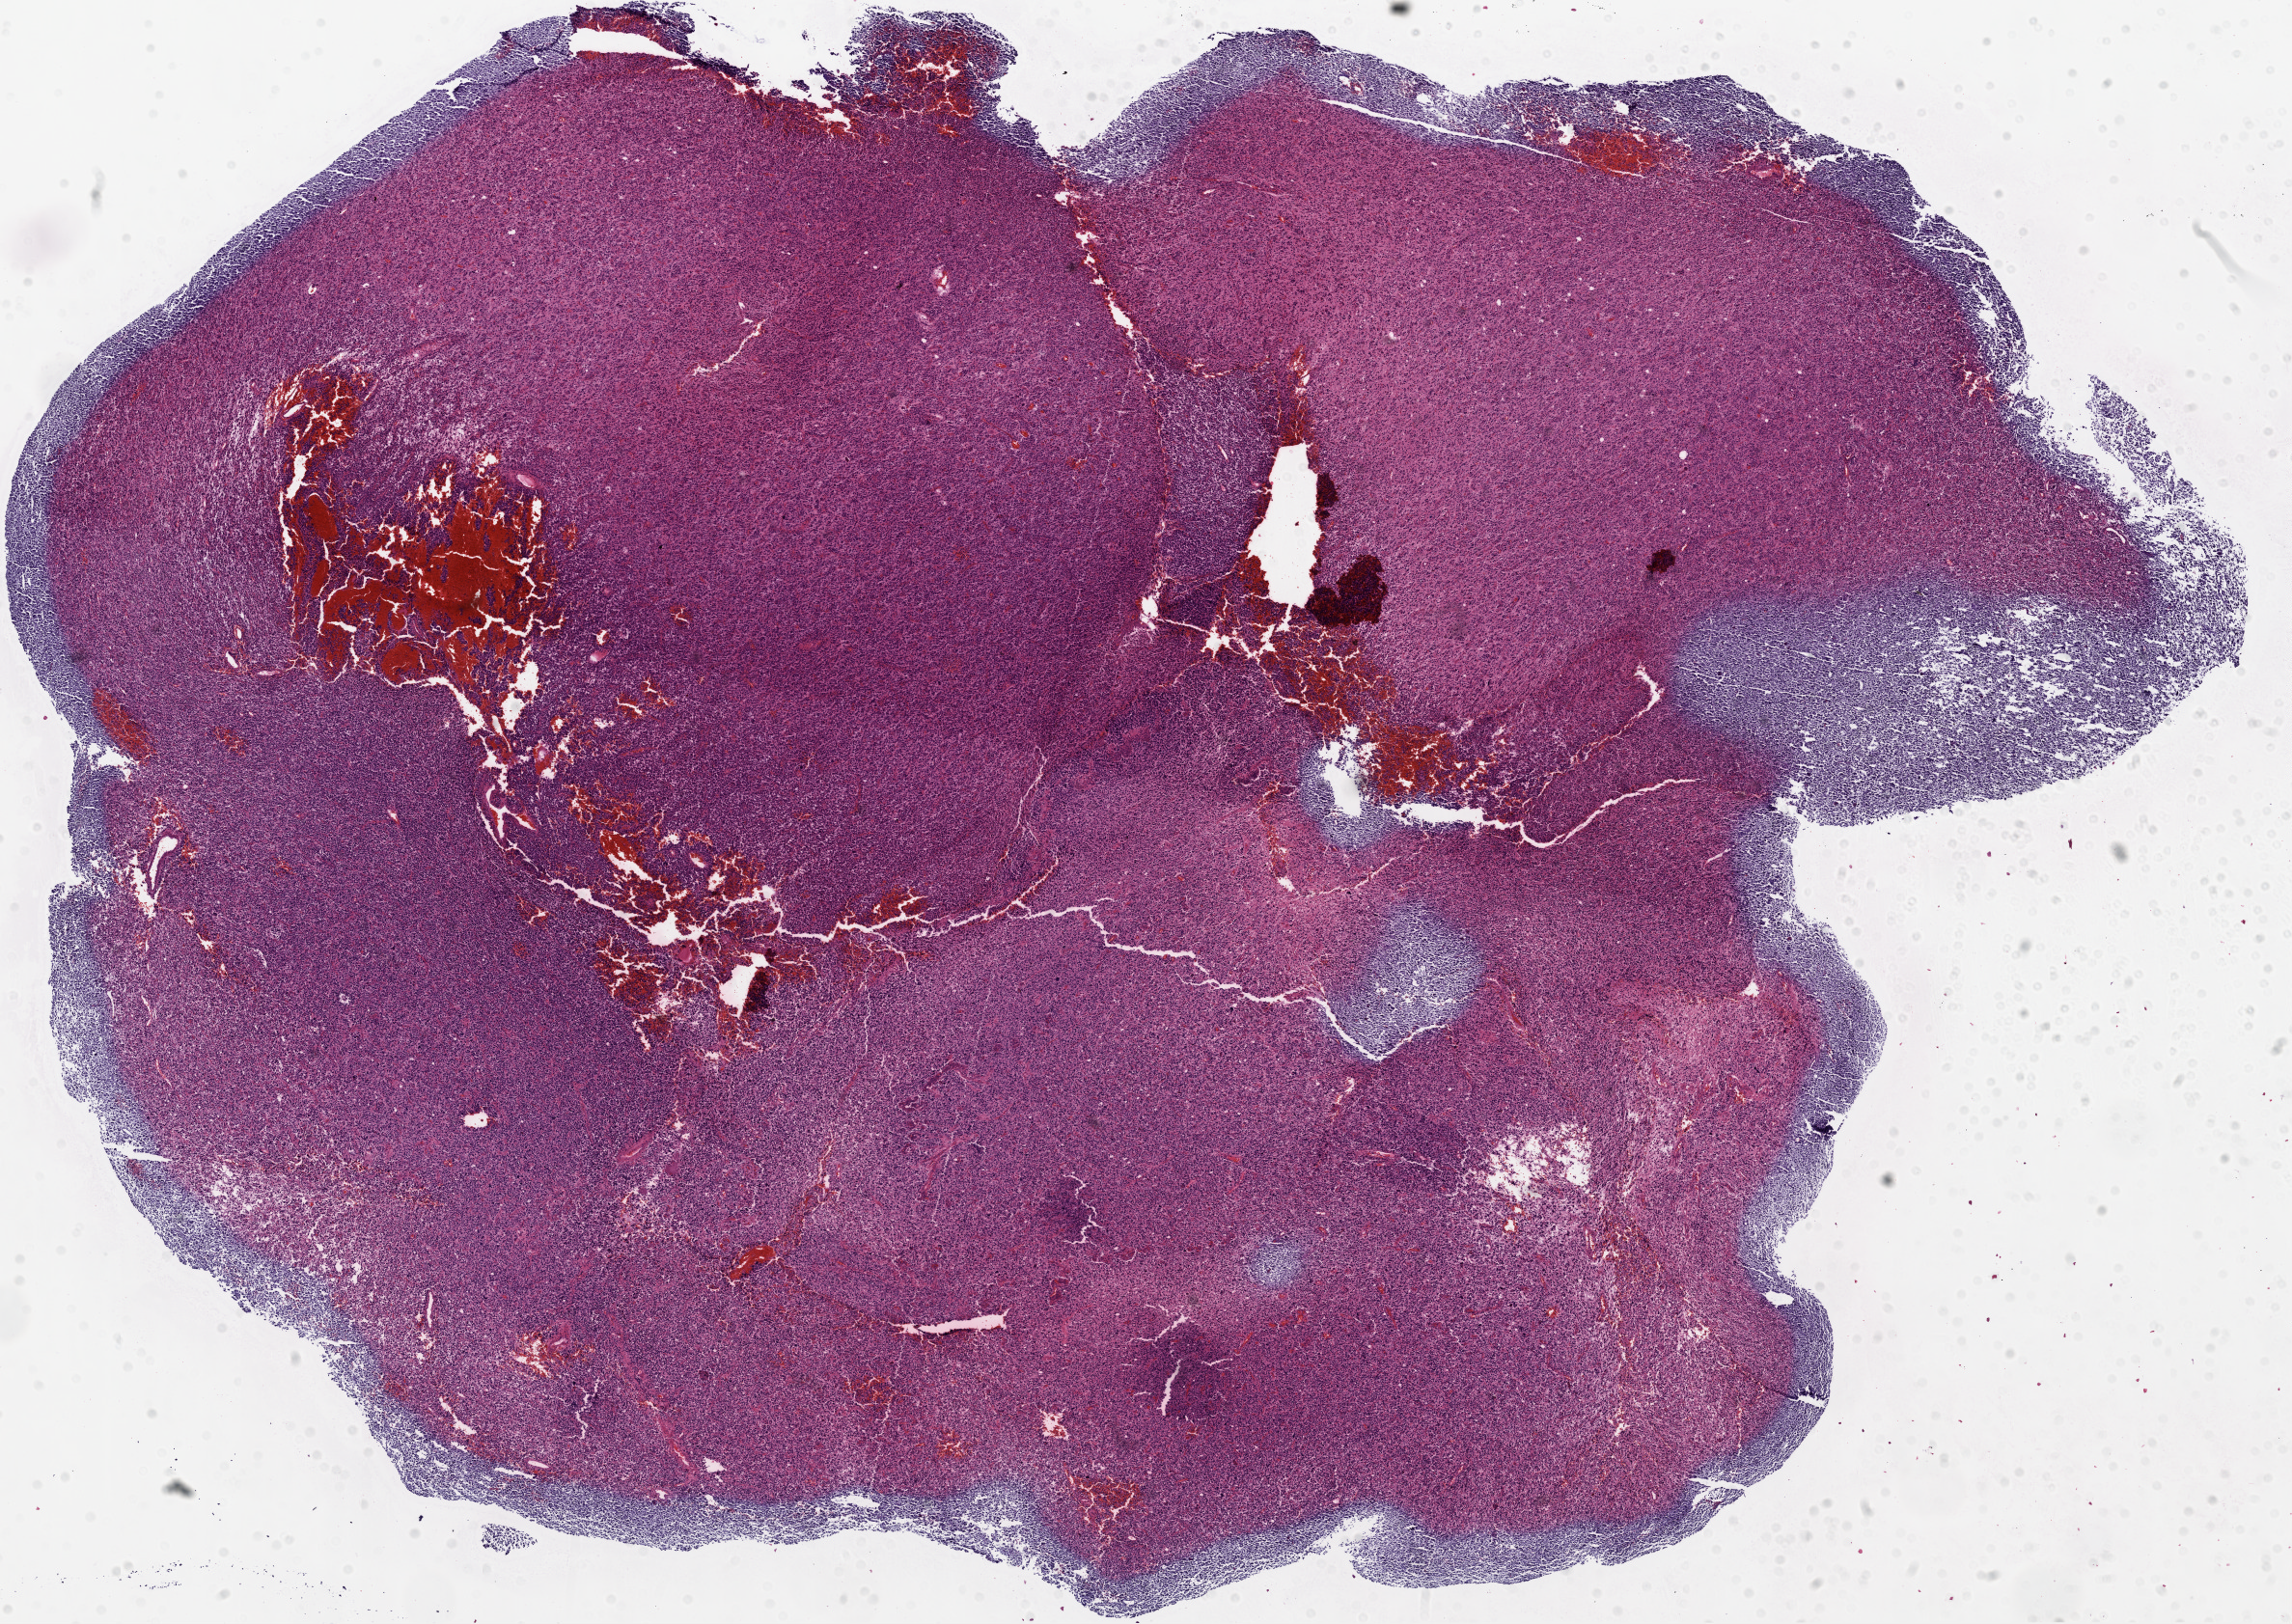
Digitized Hematoxylin and eosin (H&E) stained tissue section (whole slide) — a low-resolution overview of the entire scanned area, about 19.1 x 13.5 mm; formalin-fixed paraffin-embedded (FFPE) diagnostic section; sample: primary tumour, brain. Patient: female, age at initial diagnosis 36 years.
Histologic diagnosis: Glioblastoma.